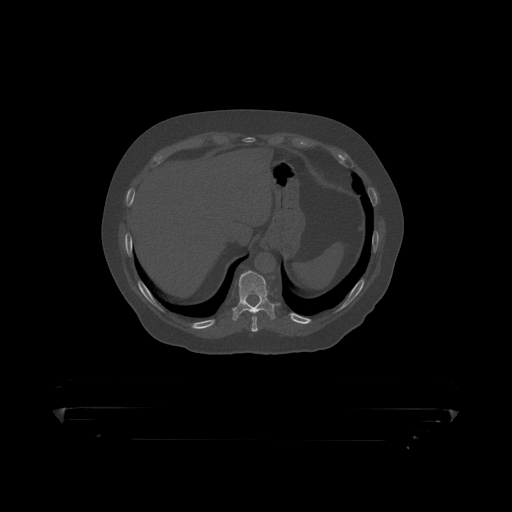
CT including the spine, one axial slice. Slice 219 of 390 in the series (ordered by position). 120 kVp. Bone window (W 1800 / L 400 HU). 1.25 mm slice thickness. 512 × 512 image matrix. Patient: male, 60 years. Case-level facts recorded for this patient, not image findings: primary cancer: prostate.
Outlined on this slice (semi-automatically segmented with operator editing):
- T10 vertebra: box from (x=233, y=271) to (x=275, y=317) px
- T9 vertebra: (x=252, y=316)–(x=258, y=319)